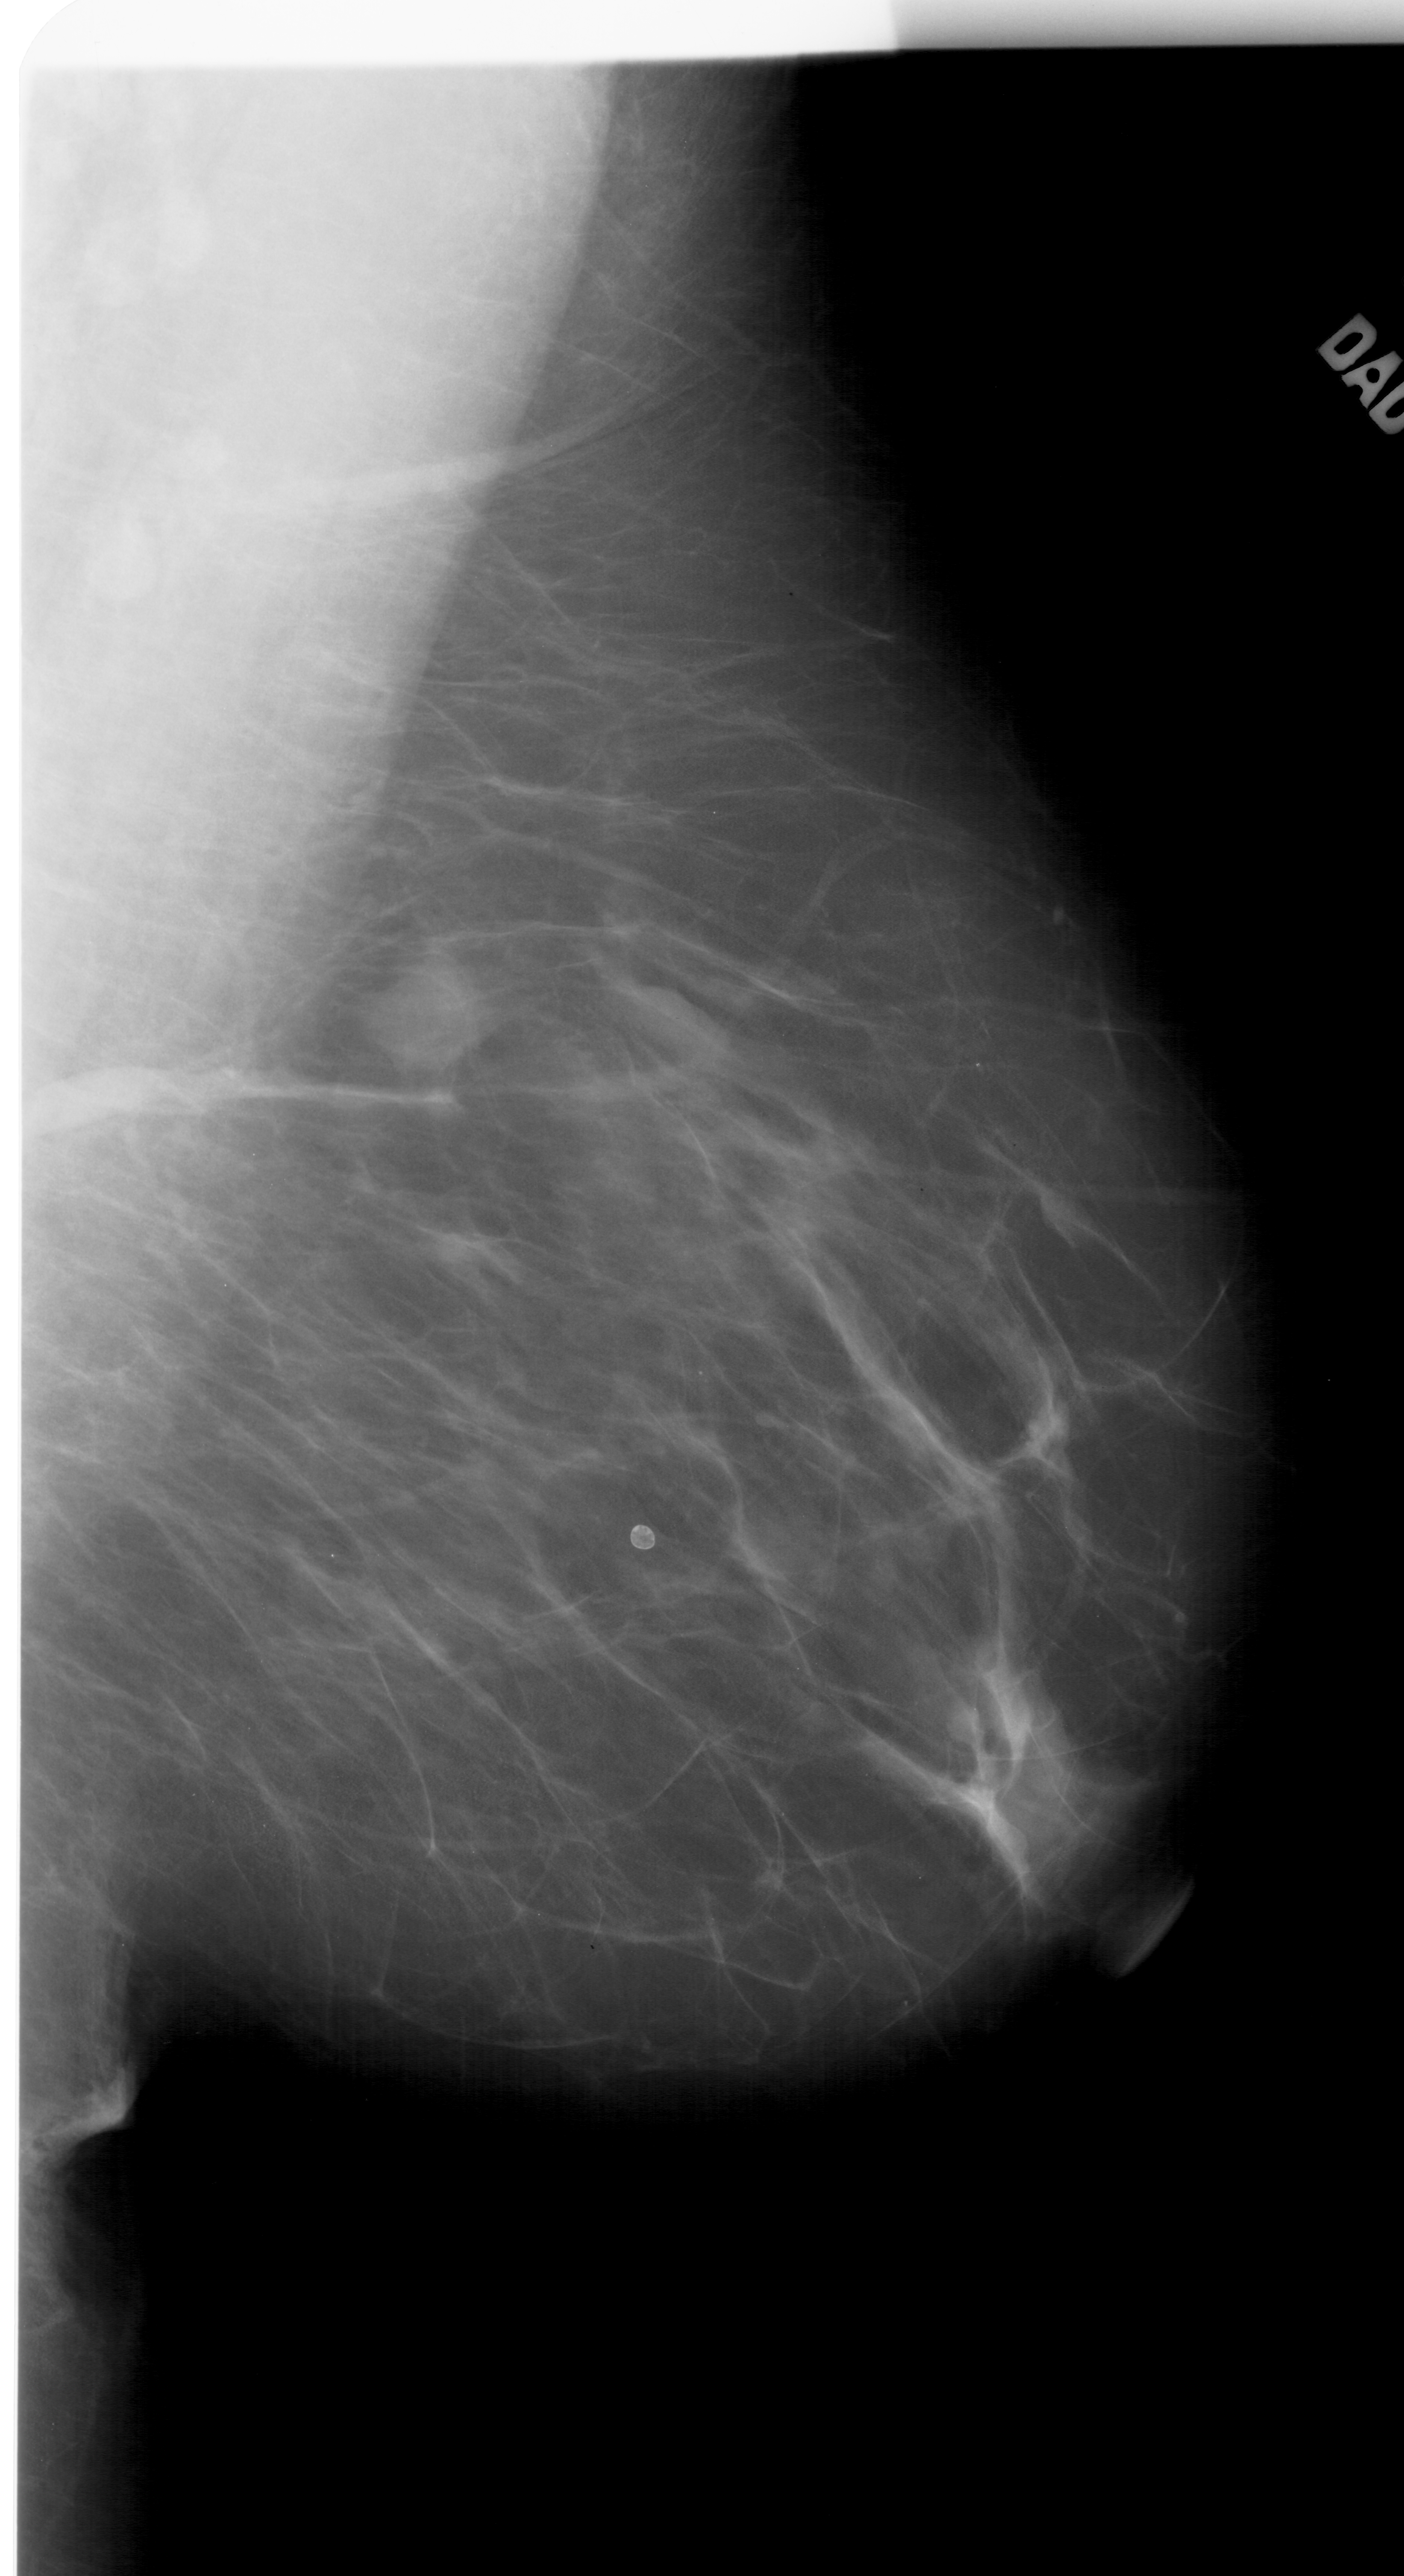
Scanned film-screen mammogram. Right breast. Mediolateral oblique (MLO) view. 1404 × 2576 image matrix.
Marked abnormalities (boxes around the expert regions of interest):
- mass, shape lobulated, margins ill defined; BI-RADS assessment category 4; subtlety rating 4 on a 1 (subtle) to 5 (obvious) scale; pathology (as recorded): benign: bounding box [x1, y1, x2, y2] px = [376, 959, 498, 1070]